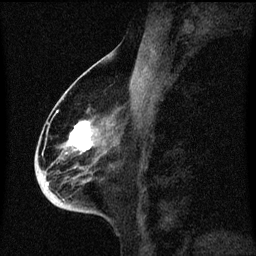
Breast MRI (dynamic contrast-enhanced), one sagittal slice; slice 32 of 60 in the series (ordered by position); dynamic contrast-enhanced series, image 2 of 3 at this slice position (ordered by acquisition); 1.5 T; TE 4.2 ms, TR 8.4 ms; 2 mm slice thickness; 256 × 256 image matrix, field of view 200 × 200 mm. Patient: female, 68 years. Case-level facts recorded for this patient, not image findings: setting: breast cancer imaged before/during neoadjuvant chemotherapy; receptor status: triple-negative.
Structures marked on this image (semi-automatic segmentation, software-assisted and operator-edited):
- analysis volume of interest (the breast-tissue region the enhancement analysis was run in; not a lesion): bounding box <37,96,113,213> (left, top, right, bottom; pixels)
- tumour enhancement mask (voxels above the 70 % enhancement threshold inside the analysis volume of interest): <41,122,94,185>